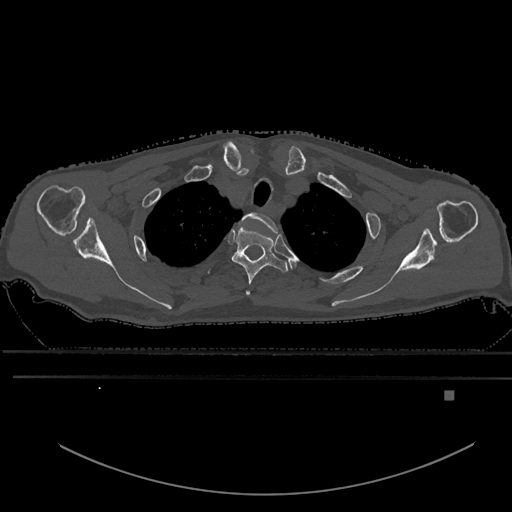
CT including the spine, one axial slice; slice 497 of 969 in the series (ordered by position); bone window (W 1800 / L 400 HU); 0.5 mm slice thickness; 512 × 512 image matrix, field of view 456 × 456 mm. Patient: male, 82 years. From the clinical record (not read from this slice): primary cancer: prostate; vertebrae with lytic lesions (as recorded): T11, T9, T8, T2.
Structures marked on this image (semi-automatic segmentation, software-assisted and operator-edited):
- T1 vertebra: box from (x=243, y=212) to (x=278, y=233) px
- T2 vertebra: (x=231, y=225)–(x=288, y=295)